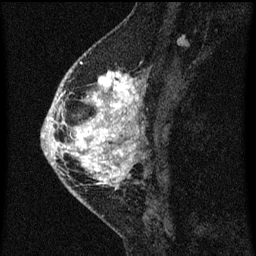
Breast MRI (dynamic contrast-enhanced), one sagittal slice; slice 26 of 60 in the series (ordered by position); dynamic contrast-enhanced series, image 2 of 3 at this slice position (ordered by acquisition); 1.5 T; TE 4.2 ms, TR 8 ms; 256 × 256 image matrix, field of view 180 × 180 mm. Patient: female, 46 years.
Structures marked on this image (semi-automatic segmentation, software-assisted and operator-edited):
- analysis volume of interest (the breast-tissue region the enhancement analysis was run in; not a lesion): bounding box (x1, y1, x2, y2) in pixels: (48, 68, 145, 195)
- tumour enhancement mask (voxels above the 70 % enhancement threshold inside the analysis volume of interest): (48, 70, 144, 189)